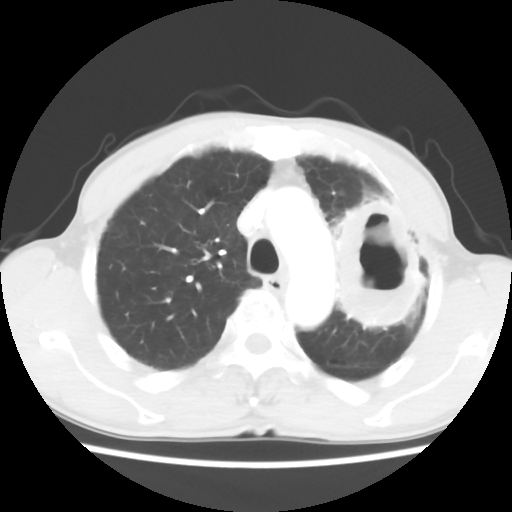
Chest CT, one axial slice. Slice 44 of 60 in the series (ordered by position). Reconstruction kernel STANDARD. 120 kVp. Lung window (W 1500 / L -600 HU). 512 × 512 image matrix, field of view 308 × 308 mm. Patient: male, 64 years. Case-level facts recorded for this patient, not image findings: clinical TNM (as recorded): T3 N3 M0.
Annotated regions visible in this slice (bounding box drawn by a radiologist):
- lung tumour (recorded histology: adenocarcinoma): bounding box [x1, y1, x2, y2] px = [312, 183, 432, 344]